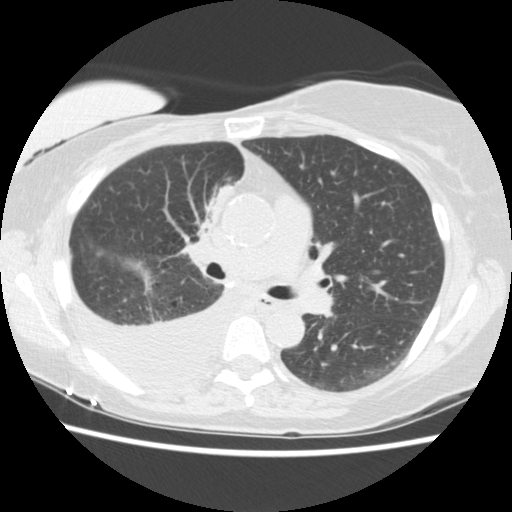
Low-dose screening chest CT, axial slice. Third screening round (two years after baseline). Lung window (W 1500 / L -600 HU). 2.5 mm slice thickness. Slice 69 of 157 in the series. 512 × 512 image matrix. Female participant, aged 56 years at enrolment. Current smoker at enrolment.
Expert-annotated lung lesion, bounding box (x1, y1, x2, y2) in pixels: (184, 173, 248, 240). The screening reader recorded 2 non-calcified nodules or masses ≥4 mm on this exam (right middle lobe, right lower lobe); which of them this box marks is not recorded. Participant outcome: lung cancer diagnosed 160 days after this screen — adenocarcinoma, NOS, right upper lobe, stage IIIB (AJCC 6th edition), 8 mm at pathology.